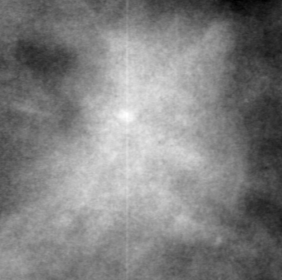
Cropped region of a digitized screen-film mammogram centred on a radiologist-marked abnormality; left breast; MLO view.
Finding: mass, shape focal asymmetric density, margins ill defined; BI-RADS assessment category 4; subtlety rating 3 on a 1 (subtle) to 5 (obvious) scale; pathology (as recorded): malignant.